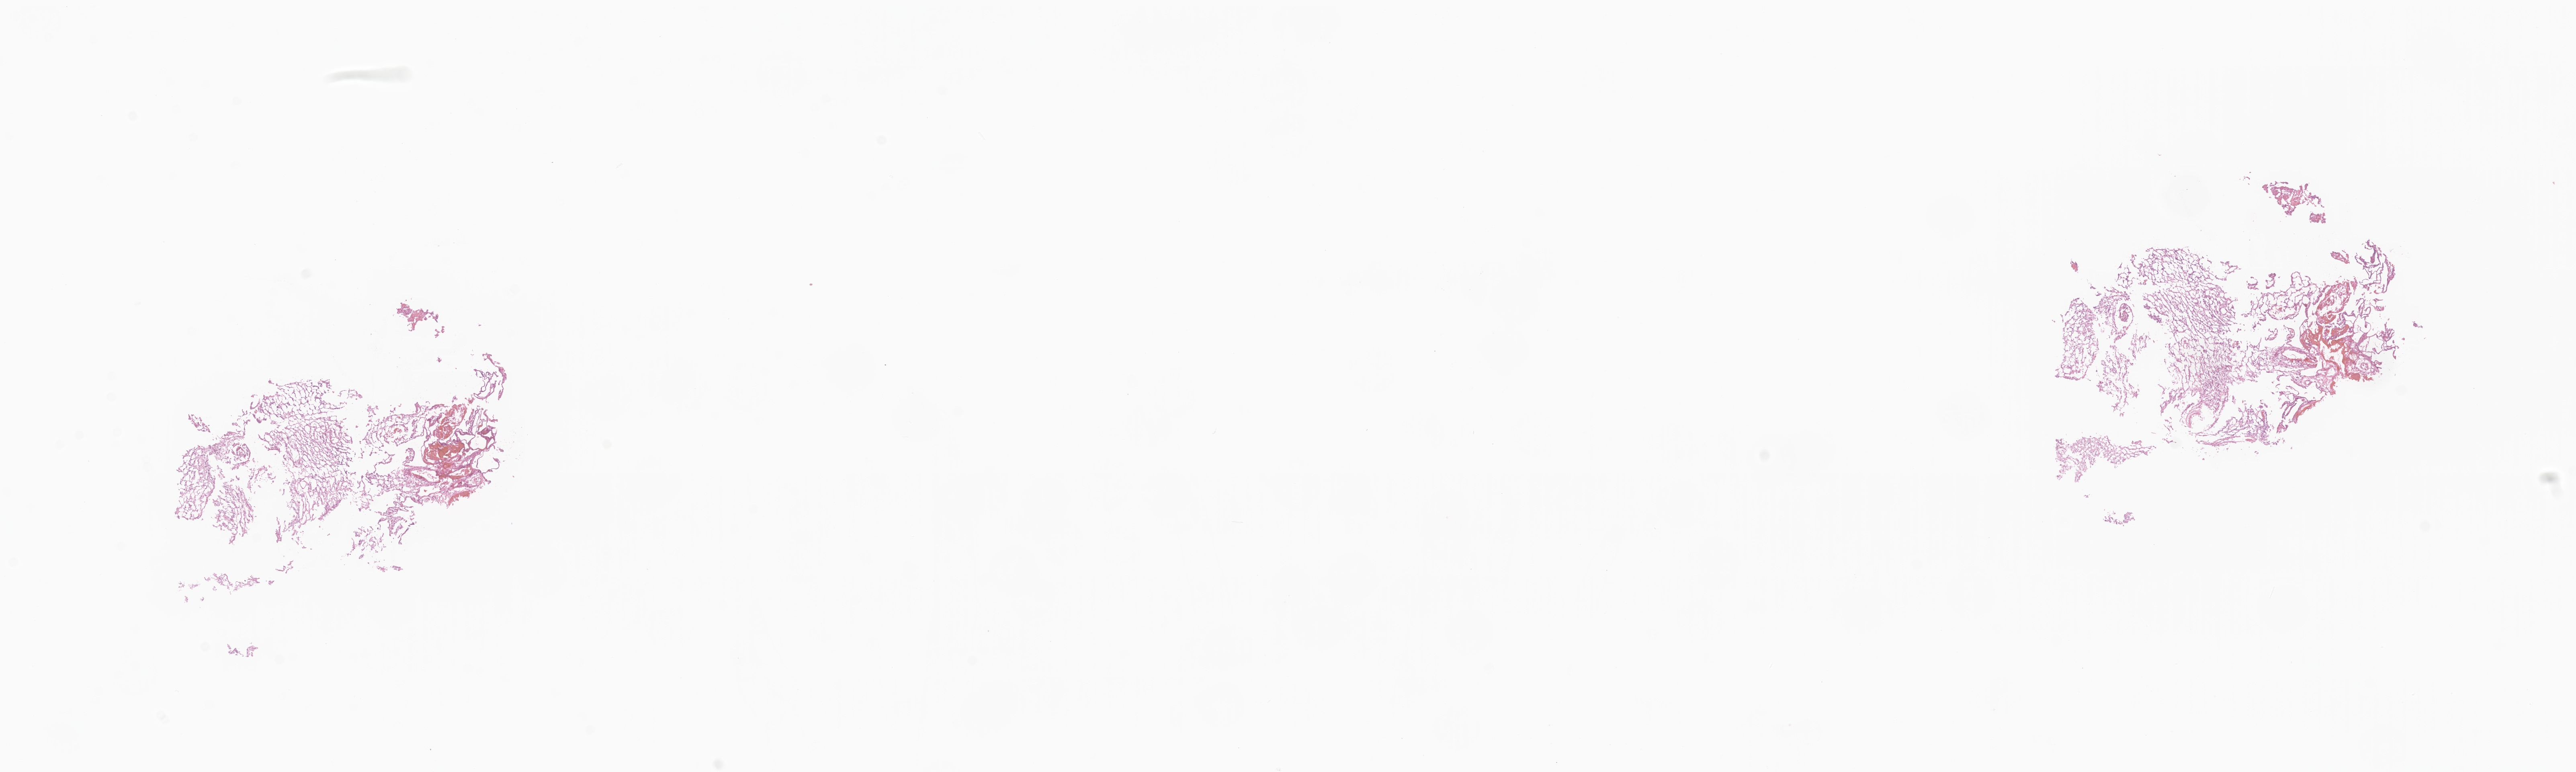
Whole-slide image, haematoxylin and eosin stain of tumor tissue from the brain — low-resolution overview of the scanned area, about 27.0 x 8.1 mm, frozen section (OCT-embedded). Patient: male, age 515 days (about 1.4 years).
Diagnosis: Ependymoma, NOS.